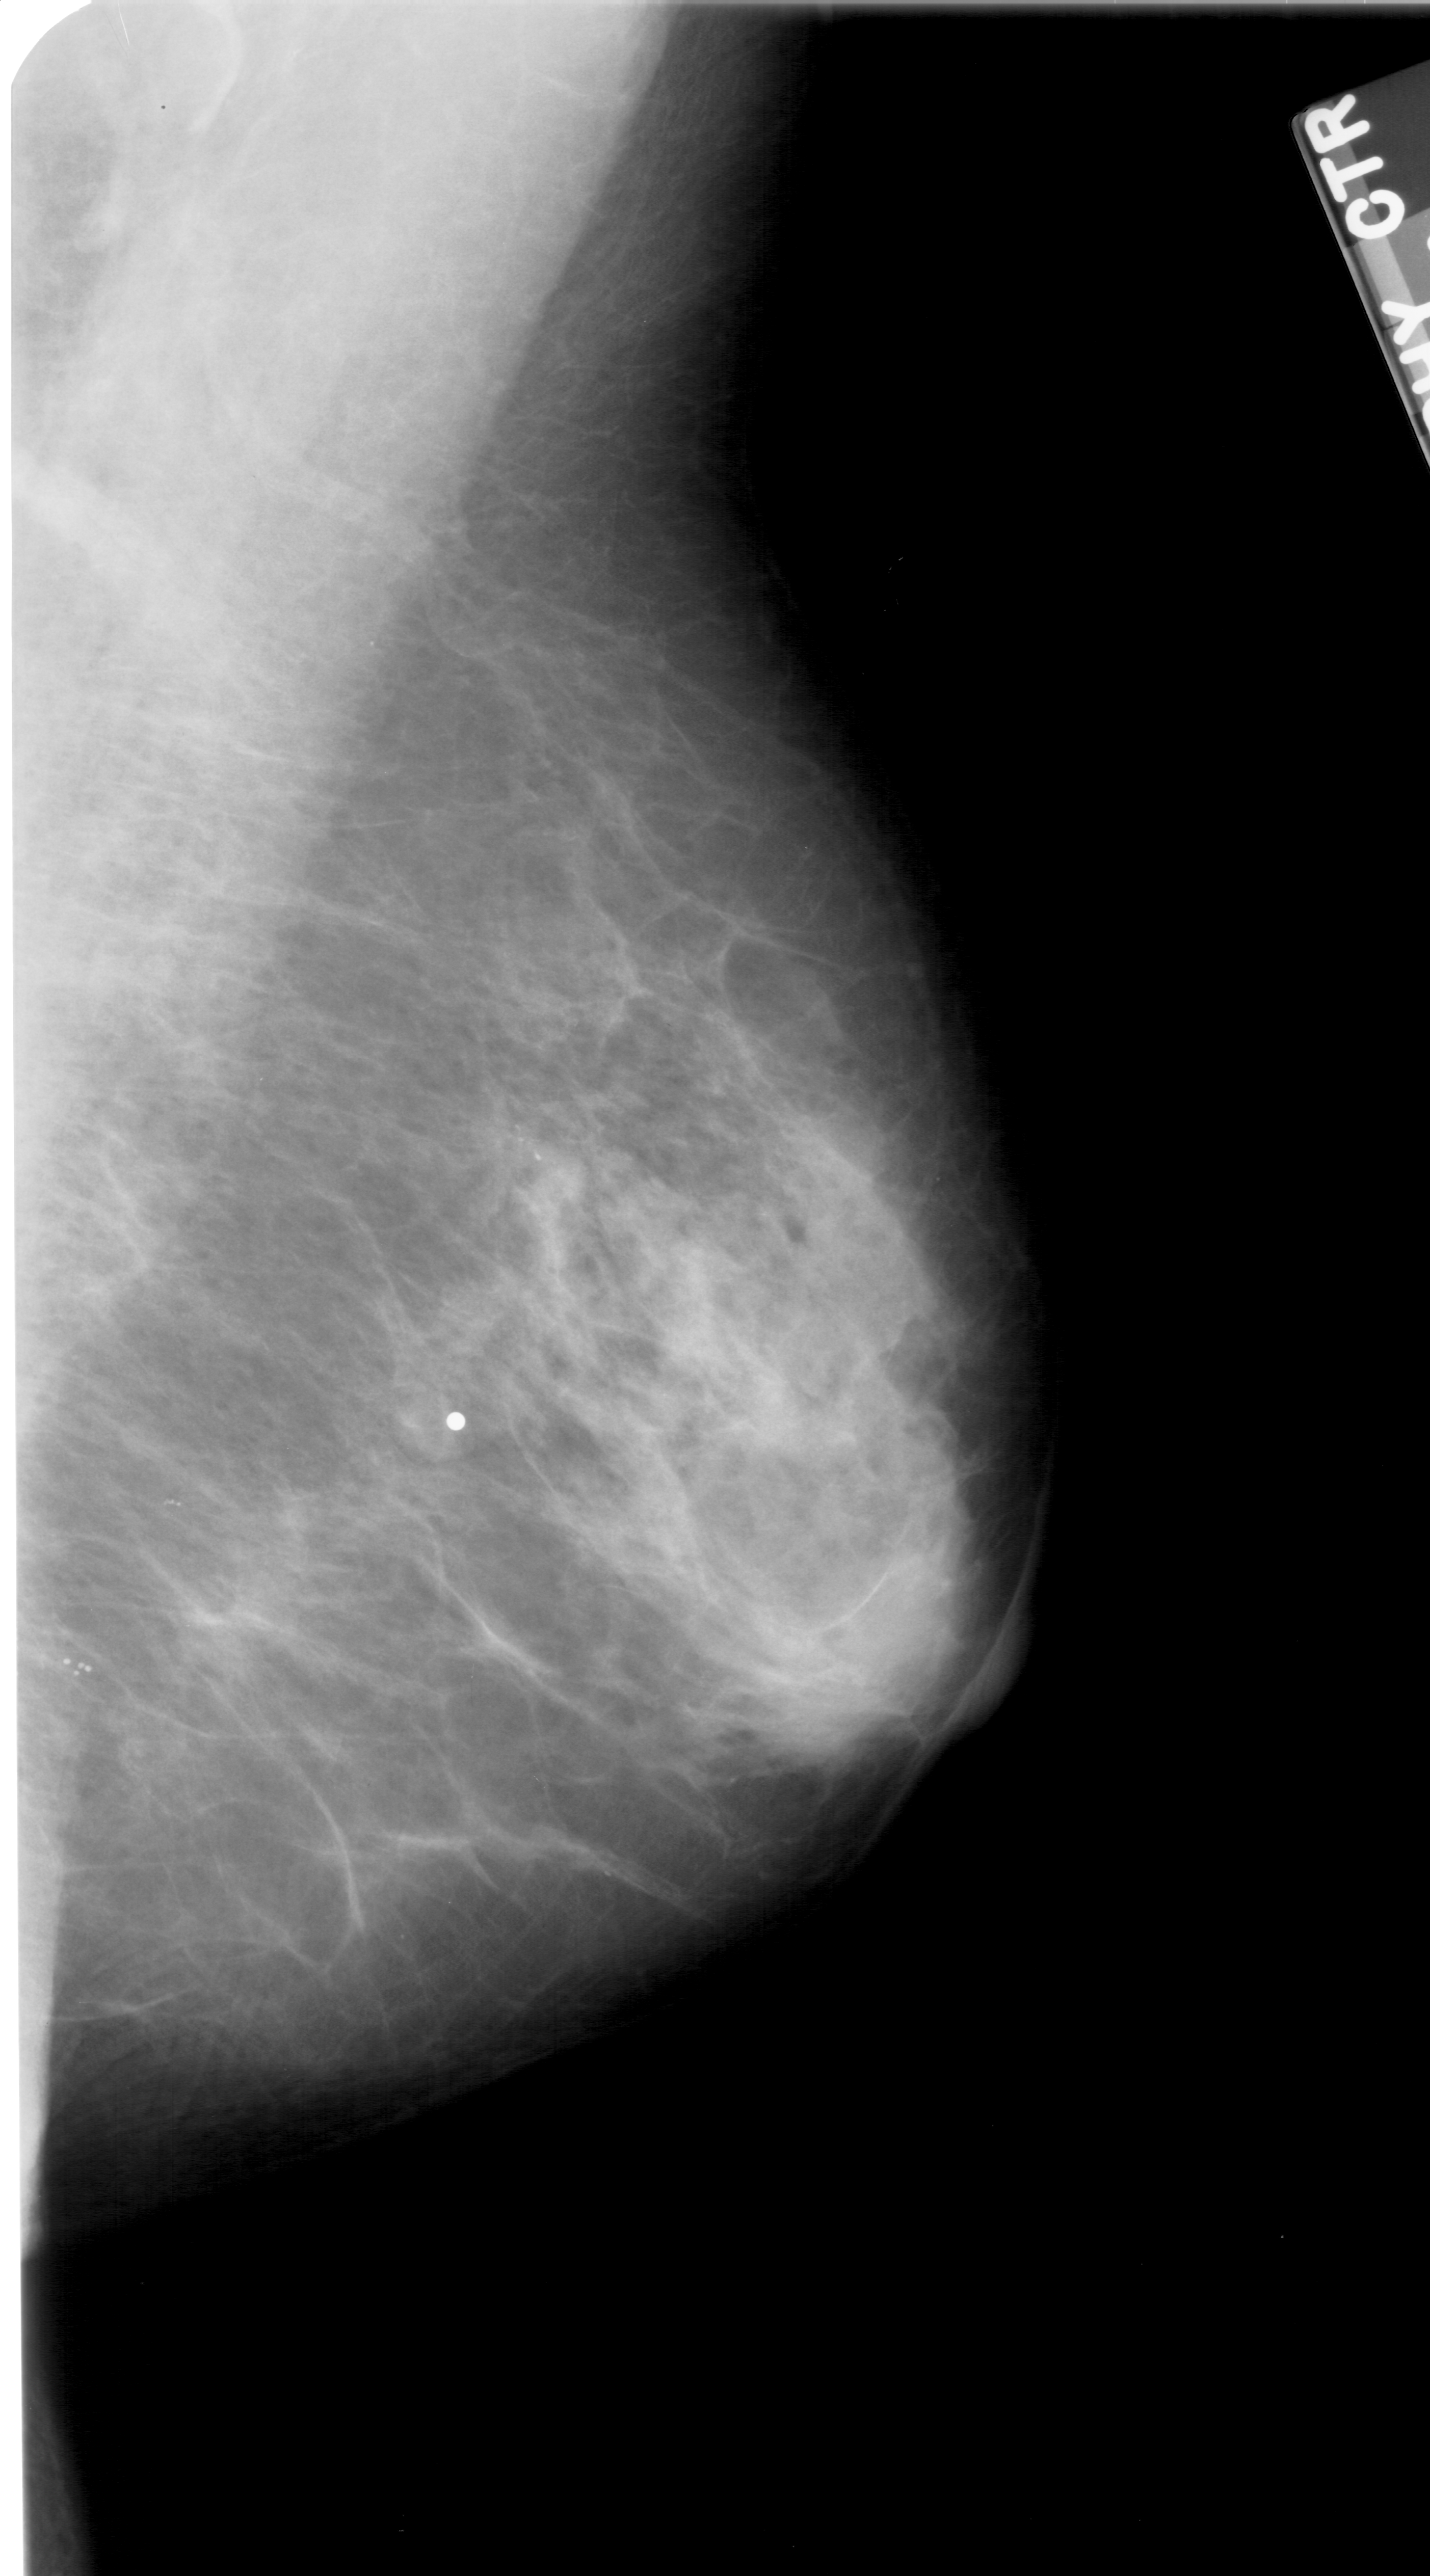
Mammogram (digitized film), right breast, mediolateral oblique (MLO) view, breast composition: scattered fibroglandular densities (BI-RADS density category 2 of 4).
Finding: calcifications, morphology pleomorphic, distribution clustered; BI-RADS assessment category 4; pathology result (as recorded, not read from the image): malignant.